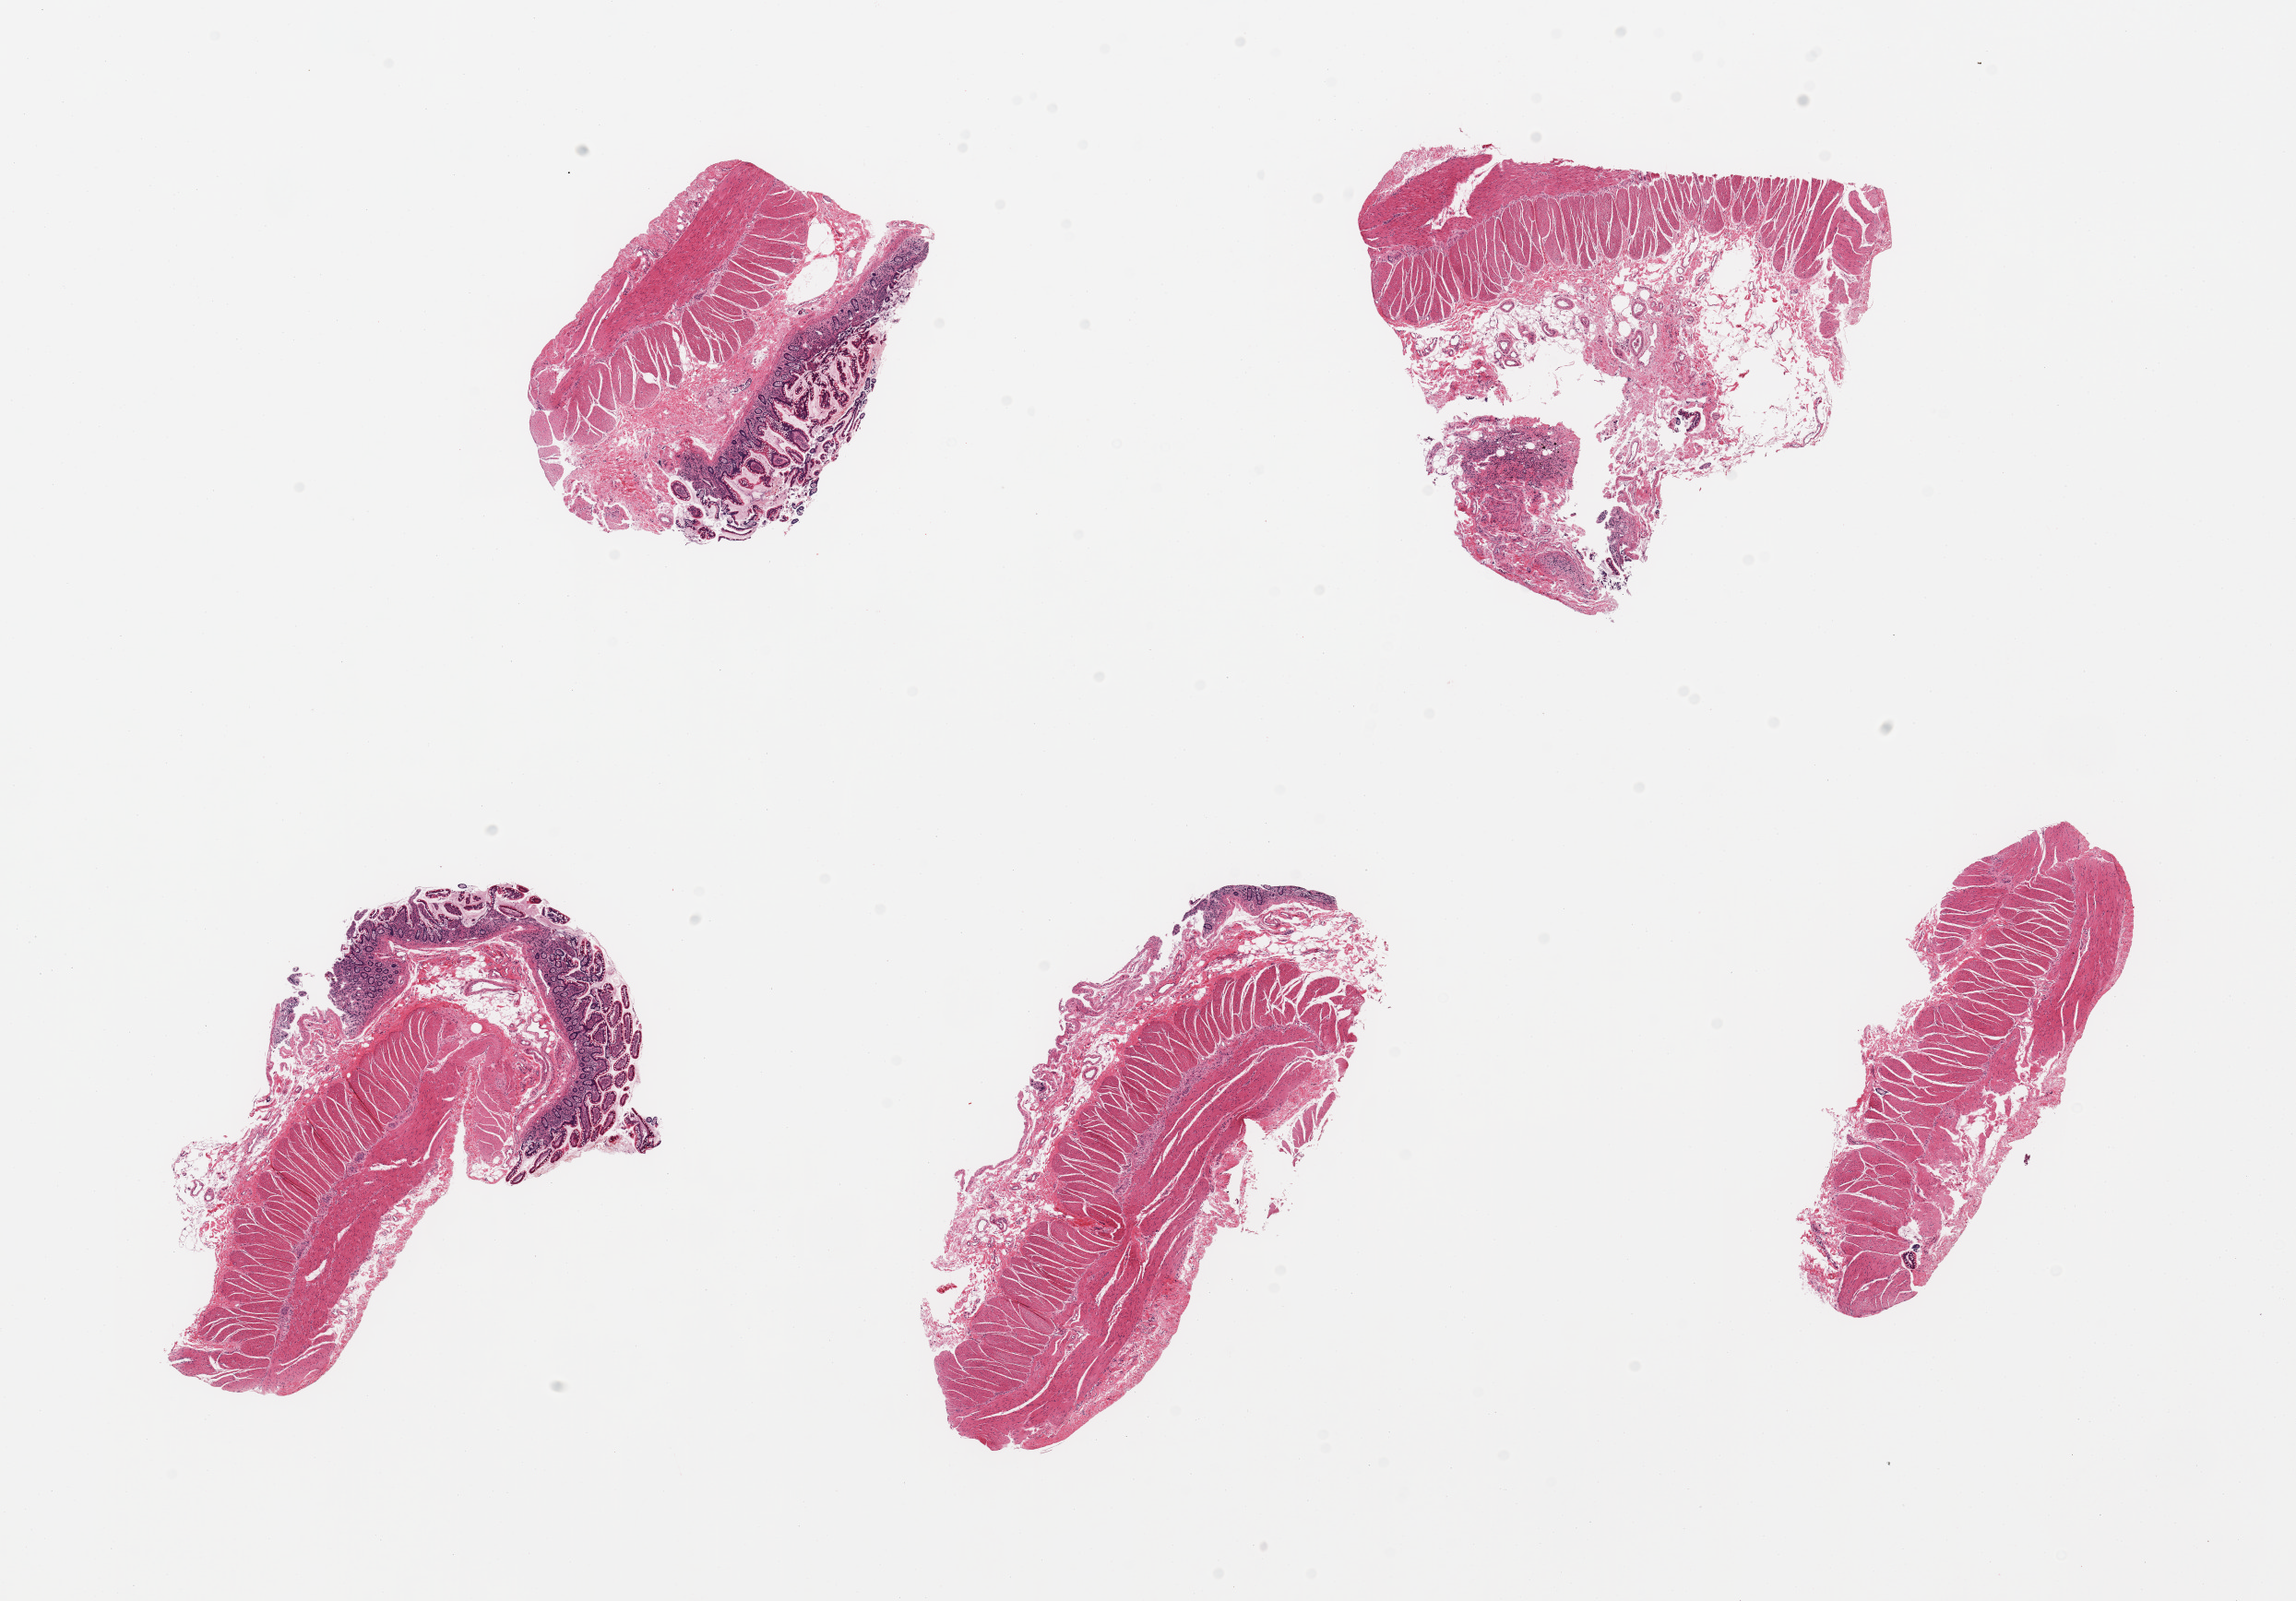
H&E whole-slide image — low-resolution overview of the scanned area, about 19.7 x 13.7 mm. PAXgene-fixed paraffin-embedded (PFPE) section. Section of ileum (target tissue). Donor tissue sample. Donor: male.
- reviewer comment on this tissue sample: 6 pieces; insufficient lymphoid tissue; all contain full thickness muscularis [not target]